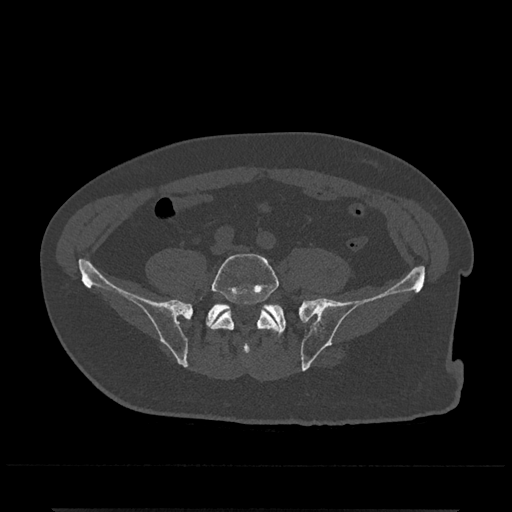
CT including the spine, one axial slice; position 70 of 797 along the scan axis; reconstruction kernel Br40s/3; 120 kVp; bone window (W 1800 / L 400 HU); 512 × 512 image matrix, field of view 393 × 393 mm. Patient: male, 67 years. From the clinical record (not read from this slice): primary cancer: prostate.
Structures marked on this image (semi-automatic segmentation, software-assisted and operator-edited):
- L5 vertebra: bounding box (x1, y1, x2, y2) in pixels: (201, 253, 279, 356)